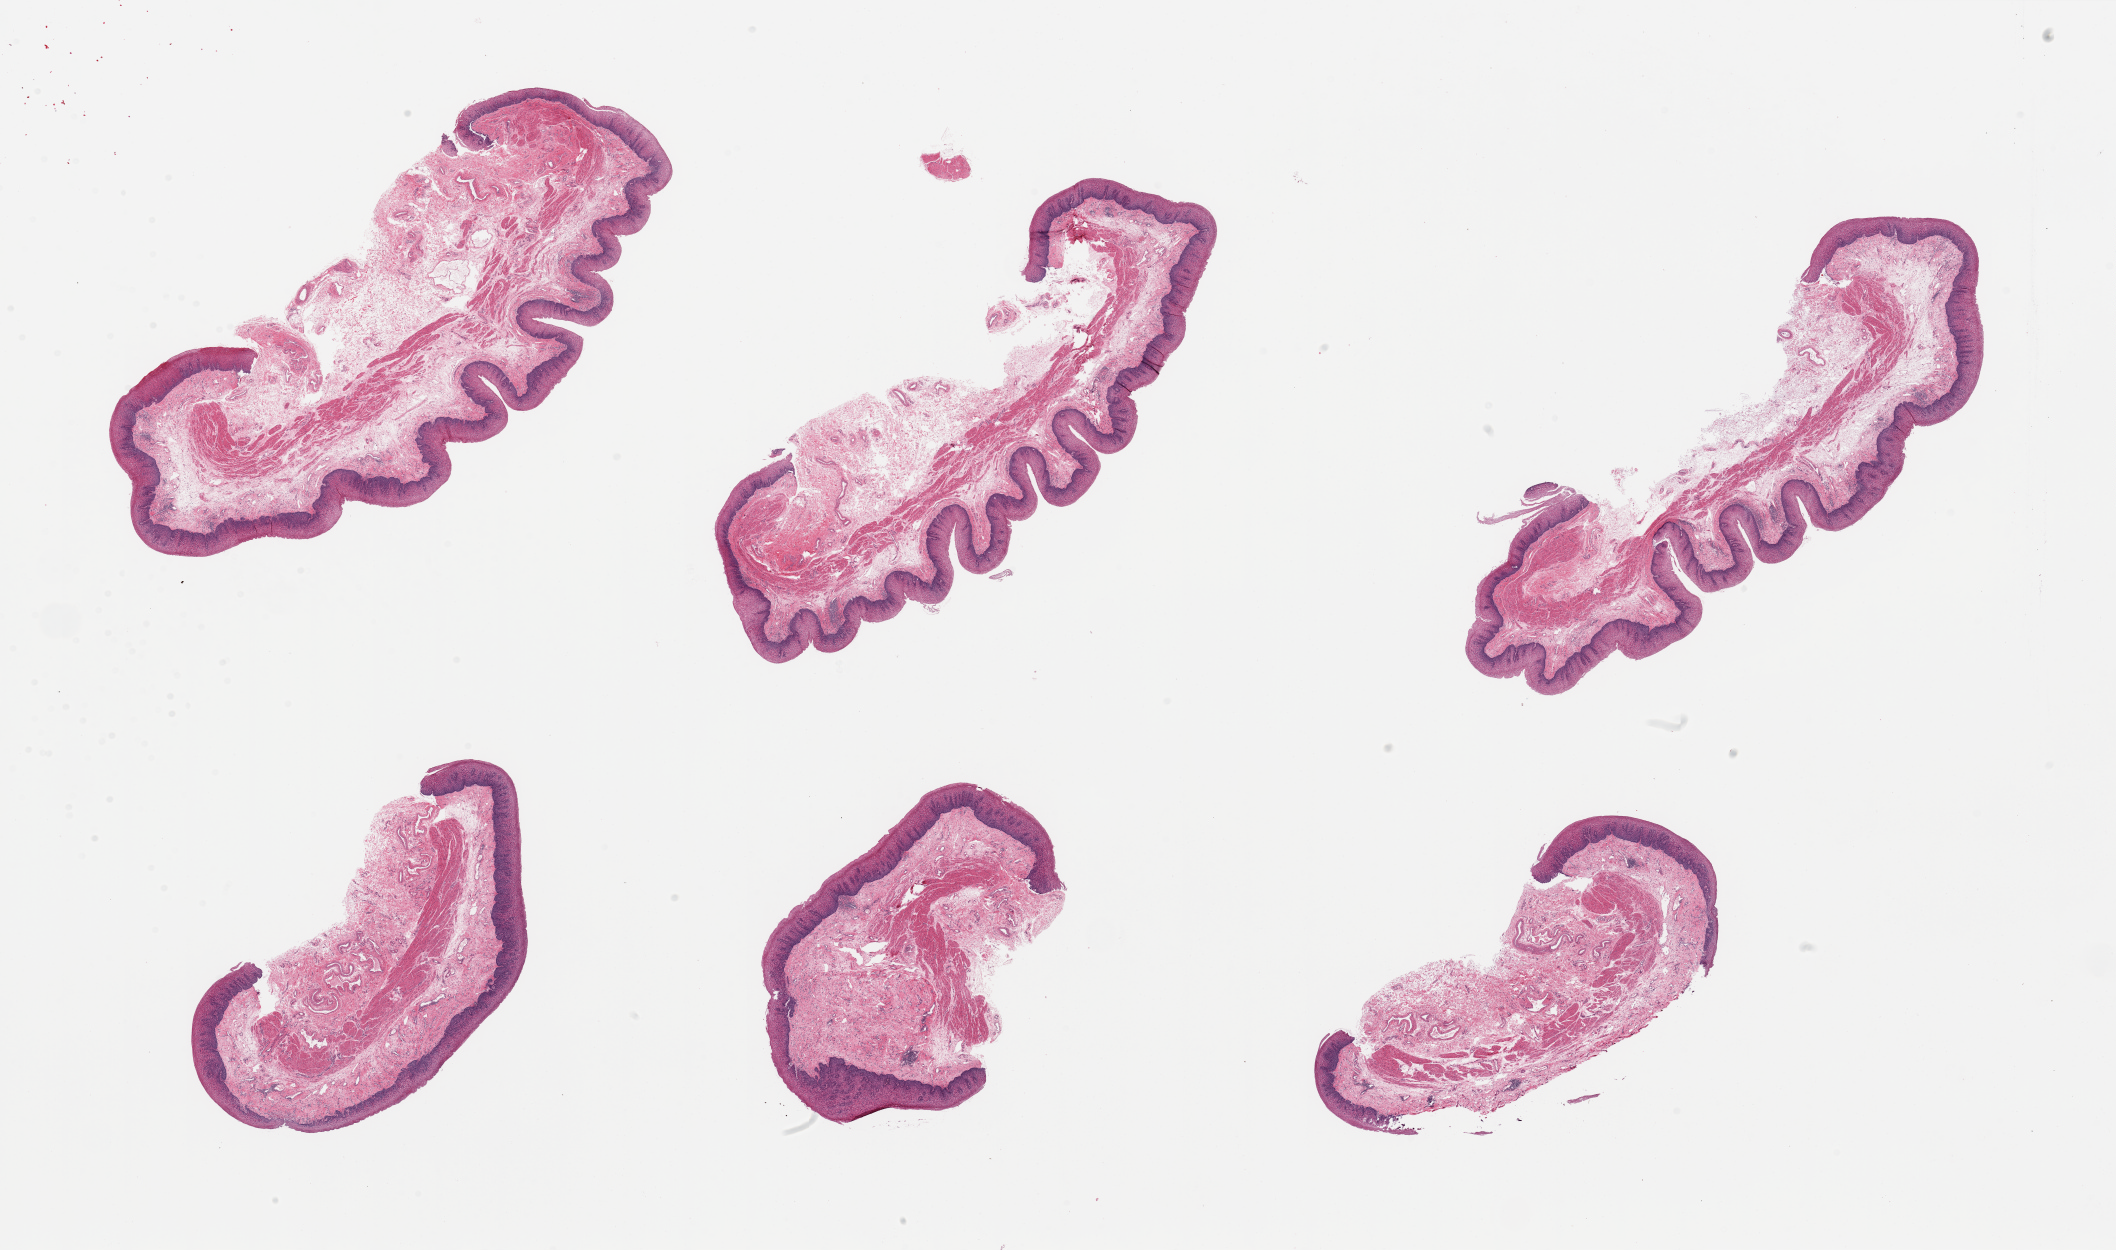
Whole-slide image, H&E stain — shown as a low-resolution overview of the whole scanned area (about 33.5 x 19.8 mm). PAXgene-fixed paraffin-embedded (PFPE) section. Sampled site (target tissue): esophageal mucous membrane. Donor tissue sample. Male donor.
Pathologist's review note for this sample: 6 pieces; eosinophilic squamous surface may indicate significant alcohol ingestion.